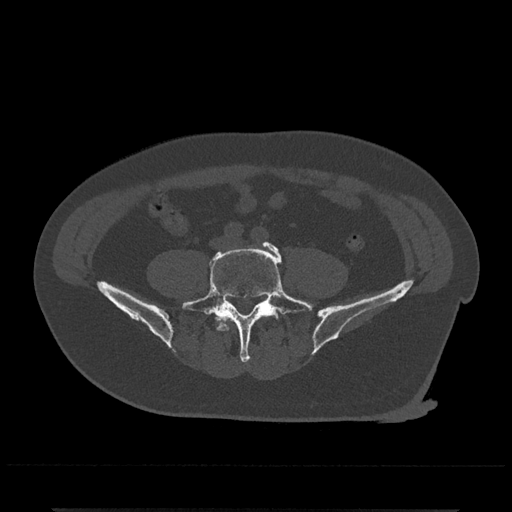
CT including the spine, one axial slice; slice 93 of 797 in the series (ordered by position); 120 kVp; bone window (W 1800 / L 400 HU); 0.5 mm slice thickness; 512 × 512 image matrix, field of view 393 × 393 mm. Patient: male, 67 years. From the clinical record (not read from this slice): primary cancer: prostate.
Structures marked on this image (semi-automatic segmentation, software-assisted and operator-edited):
- L4 vertebra: bounding box (x1, y1, x2, y2) in pixels: (220, 323, 229, 331)
- L5 vertebra: (182, 241, 313, 363)